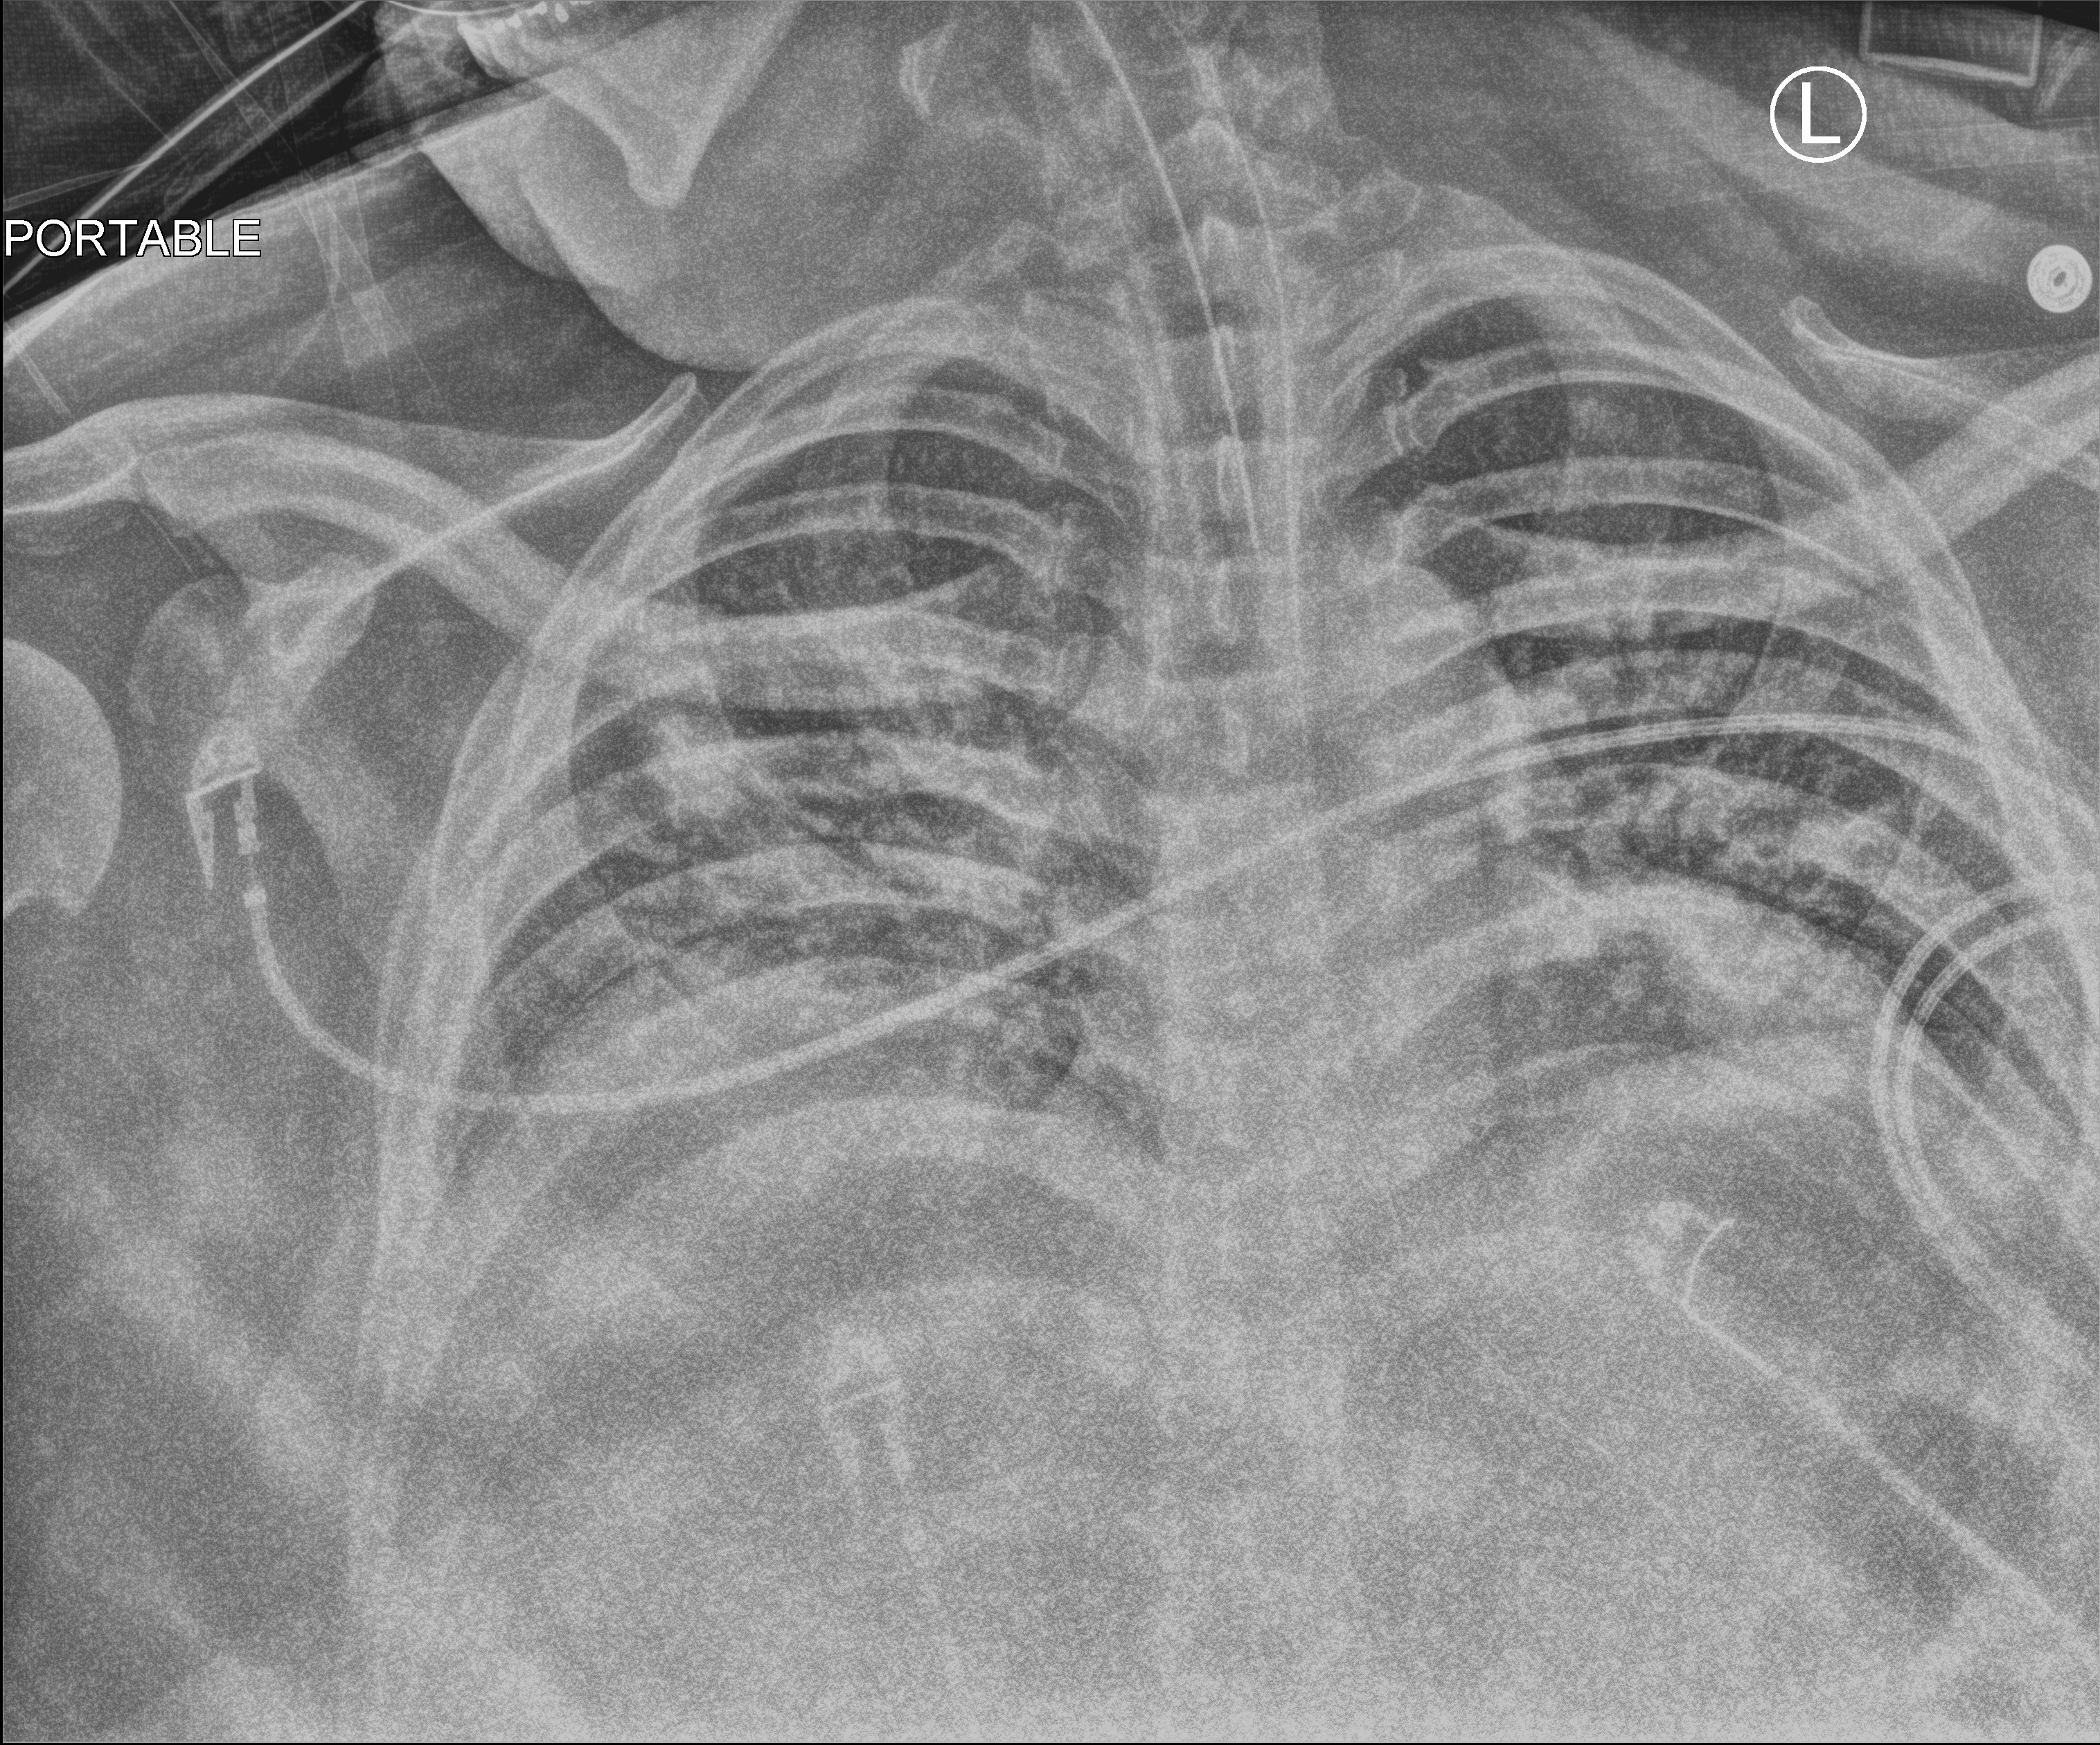
Bedside chest radiograph (computed radiography), anteroposterior (AP) projection. Patient hospitalised with COVID-19; male, aged 18–59 years.
Hospital-stay facts (about this admission, not read from this image; timing relative to this image not recorded): chronic kidney disease (admission record): no; admitted to intensive care during this hospital stay: yes.